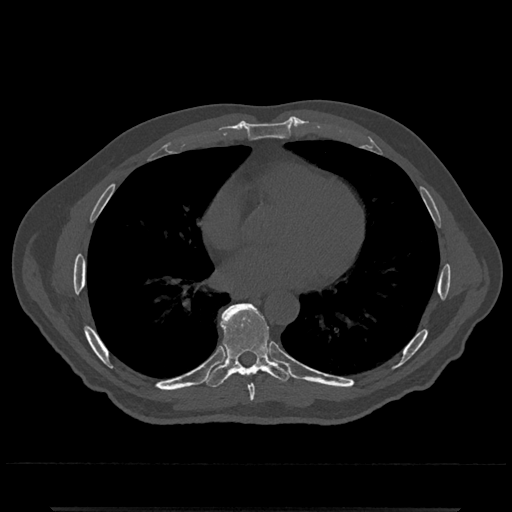
CT including the spine, one axial slice; position 683 of 797 along the scan axis; reconstruction kernel Br40s/3; 120 kVp; bone window (W 1800 / L 400 HU); 0.5 mm slice thickness; 512 × 512 image matrix. Male patient, age 67 years. From the clinical record (not read from this slice): primary cancer: prostate.
Outlined on this slice (semi-automatically segmented with operator editing):
- T7 vertebra: bounding box <248,385,255,404> (left, top, right, bottom; pixels)
- T8 vertebra: <201,304,296,388>